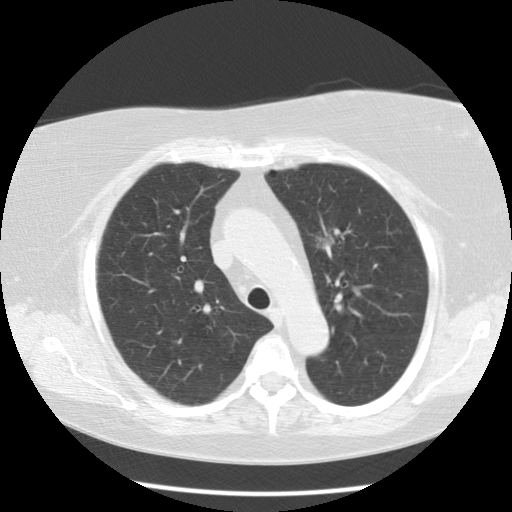
Chest CT (low-dose screening protocol), one axial image; second annual screen; lung window (W 1500 / L -600 HU); standard (soft-tissue) reconstruction kernel (STANDARD); 120 kVp. Female participant, aged 67 years at enrolment. Former smoker at enrolment.
- Expert reader's lesion annotation, bounding box <292,216,354,270> (left, top, right, bottom; pixels).
- Screening reader's record for this exam (one nodule recorded; not confirmed to be the boxed lesion): non-calcified nodule or mass ≥4 mm, left upper lobe, 20 × 18 mm, poorly defined margins, soft tissue attenuation, pre-existing on the prior screen: yes; interval growth: yes.
- Participant outcome: lung cancer diagnosed 28 days after this screen — adenocarcinoma, NOS, left upper lobe, moderately differentiated (G2), stage IIA (AJCC 6th edition), 23 mm at pathology.